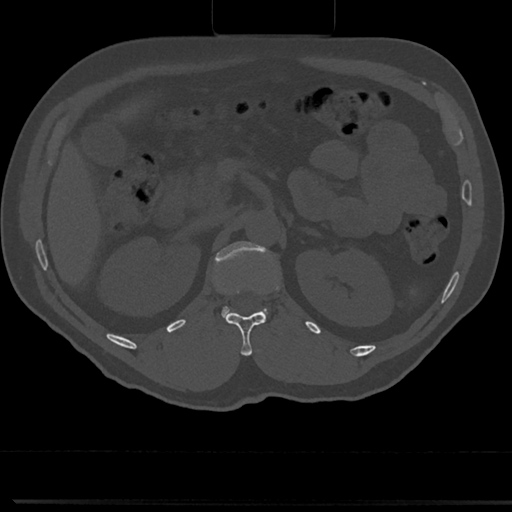
CT including the spine, one axial slice. Slice 118 of 817 in the series (ordered by position). Reconstruction kernel Br40s/3. 120 kVp. Bone window (W 1800 / L 400 HU). 0.5 mm slice thickness. 512 × 512 image matrix, field of view 355 × 355 mm. Patient: male, 61 years. Case-level facts recorded for this patient, not image findings: primary cancer: prostate.
Outlined on this slice (semi-automatically segmented with operator editing):
- L1 vertebra: box from (x=212, y=241) to (x=277, y=322) px
- T12 vertebra: (x=224, y=311)–(x=268, y=355)